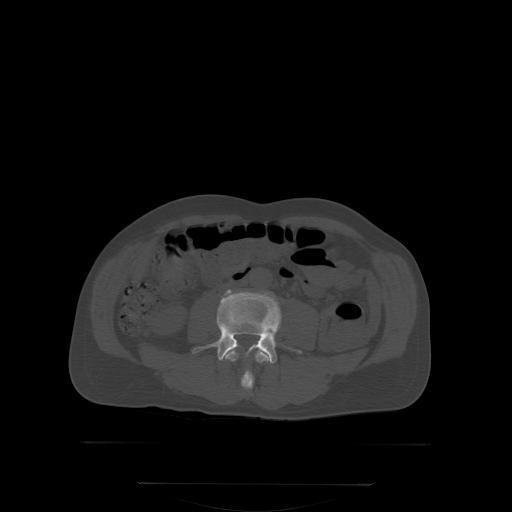
CT including the spine, one axial slice; bone window (W 1800 / L 400 HU); 2.5 mm slice thickness; 512 × 512 image matrix, field of view 500 × 500 mm. Patient: male, 58 years. From the clinical record (not read from this slice): primary cancer: prostate; vertebrae with lytic lesions (as recorded): L1.
Annotated regions visible in this slice (semi-automatically segmented with operator editing):
- L3 vertebra: bounding box [x1, y1, x2, y2] px = [227, 350, 268, 389]
- L4 vertebra: [192, 292, 302, 362]